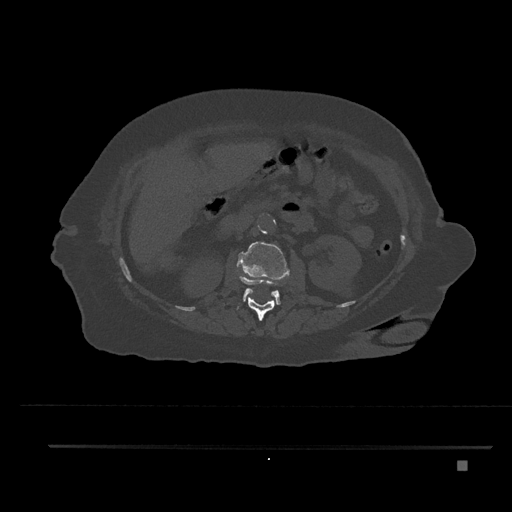
CT including the spine, one axial slice. Position 205 of 797 along the scan axis. Reconstruction kernel Br40s/3. 120 kVp. Bone window (W 1800 / L 400 HU). 0.5 mm slice thickness. 512 × 512 image matrix, field of view 437 × 437 mm. Patient: female, 76 years. Case-level facts recorded for this patient, not image findings: primary cancer: lung; vertebrae with lytic lesions (as recorded): T11, L3.
Annotated regions visible in this slice (semi-automatically segmented with operator editing):
- L1 vertebra: bounding box <223,274,286,321> (left, top, right, bottom; pixels)
- L2 vertebra: <237,242,290,304>